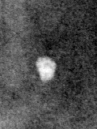
Region of interest cut from a scanned film mammogram (one marked finding); right breast; MLO view; BI-RADS breast density category 3 (scale 1–4).
- Marked abnormality: calcifications, morphology round and regular / lucent center; BI-RADS assessment category 2; benign without callback (not worked up further).